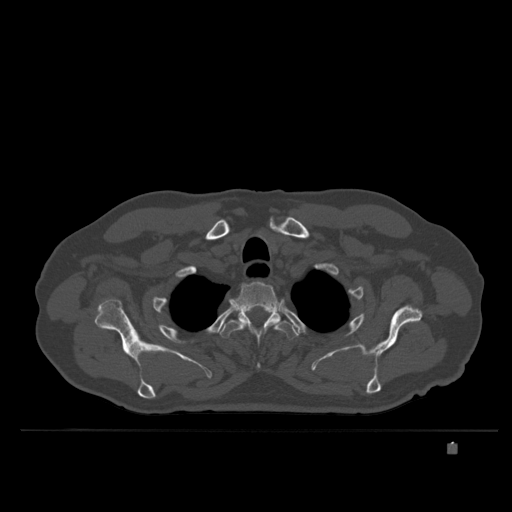
CT including the spine, one axial slice; slice 306 of 435 in the series (ordered by position); bone window (W 1800 / L 400 HU); 1.5 mm slice thickness; 512 × 512 image matrix, field of view 434 × 434 mm. Male patient, age 73 years. From the clinical record (not read from this slice): primary cancer: skin.
Outlined on this slice (semi-automatic segmentation, software-assisted and operator-edited):
- T2 vertebra: box from (x=229, y=281) to (x=281, y=331) px
- T3 vertebra: (x=219, y=308)–(x=299, y=368)